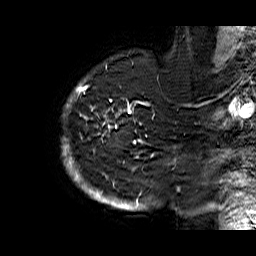
Breast MRI (dynamic contrast-enhanced), one sagittal slice. Position 53 of 60 along the scan axis. Dynamic contrast-enhanced series, time point 2 of 6 at this slice position (early post-contrast). 1.5 T. TE 6.3 ms, TR 32.9 ms. 4 mm slice thickness. 256 × 256 image matrix, field of view 200 × 200 mm. Female patient. Case-level facts recorded for this patient, not image findings: setting: breast cancer imaged before/during neoadjuvant chemotherapy; receptor status: HR-positive, HER2-negative.
Outlined on this slice (semi-automatically segmented with operator editing):
- analysis volume of interest (the breast-tissue region the enhancement analysis was run in; not a lesion): box from (x=60, y=74) to (x=176, y=210) px
- tumour enhancement mask (voxels above the 100 % enhancement threshold inside the analysis volume of interest): (x=62, y=79)–(x=173, y=210)